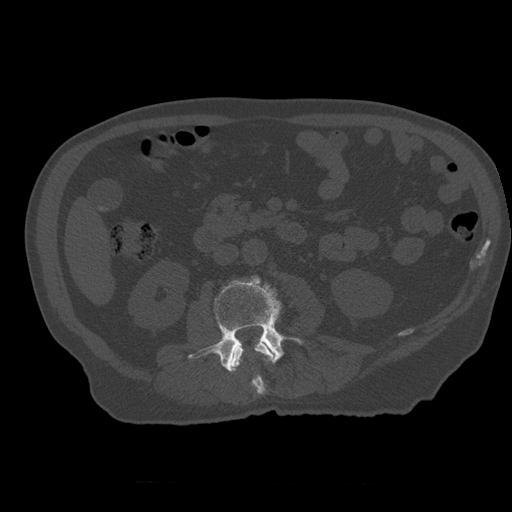
CT including the spine, one axial slice; slice 196 of 399 in the series (ordered by position); reconstruction kernel STANDARD; bone window (W 1800 / L 400 HU); 1.25 mm slice thickness; 512 × 512 image matrix. Patient age 73 years. From the clinical record (not read from this slice): primary cancer: prostate.
Outlined on this slice (semi-automatic segmentation, software-assisted and operator-edited):
- L2 vertebra: bounding box <231,341,274,395> (left, top, right, bottom; pixels)
- L3 vertebra: <188,276,302,372>